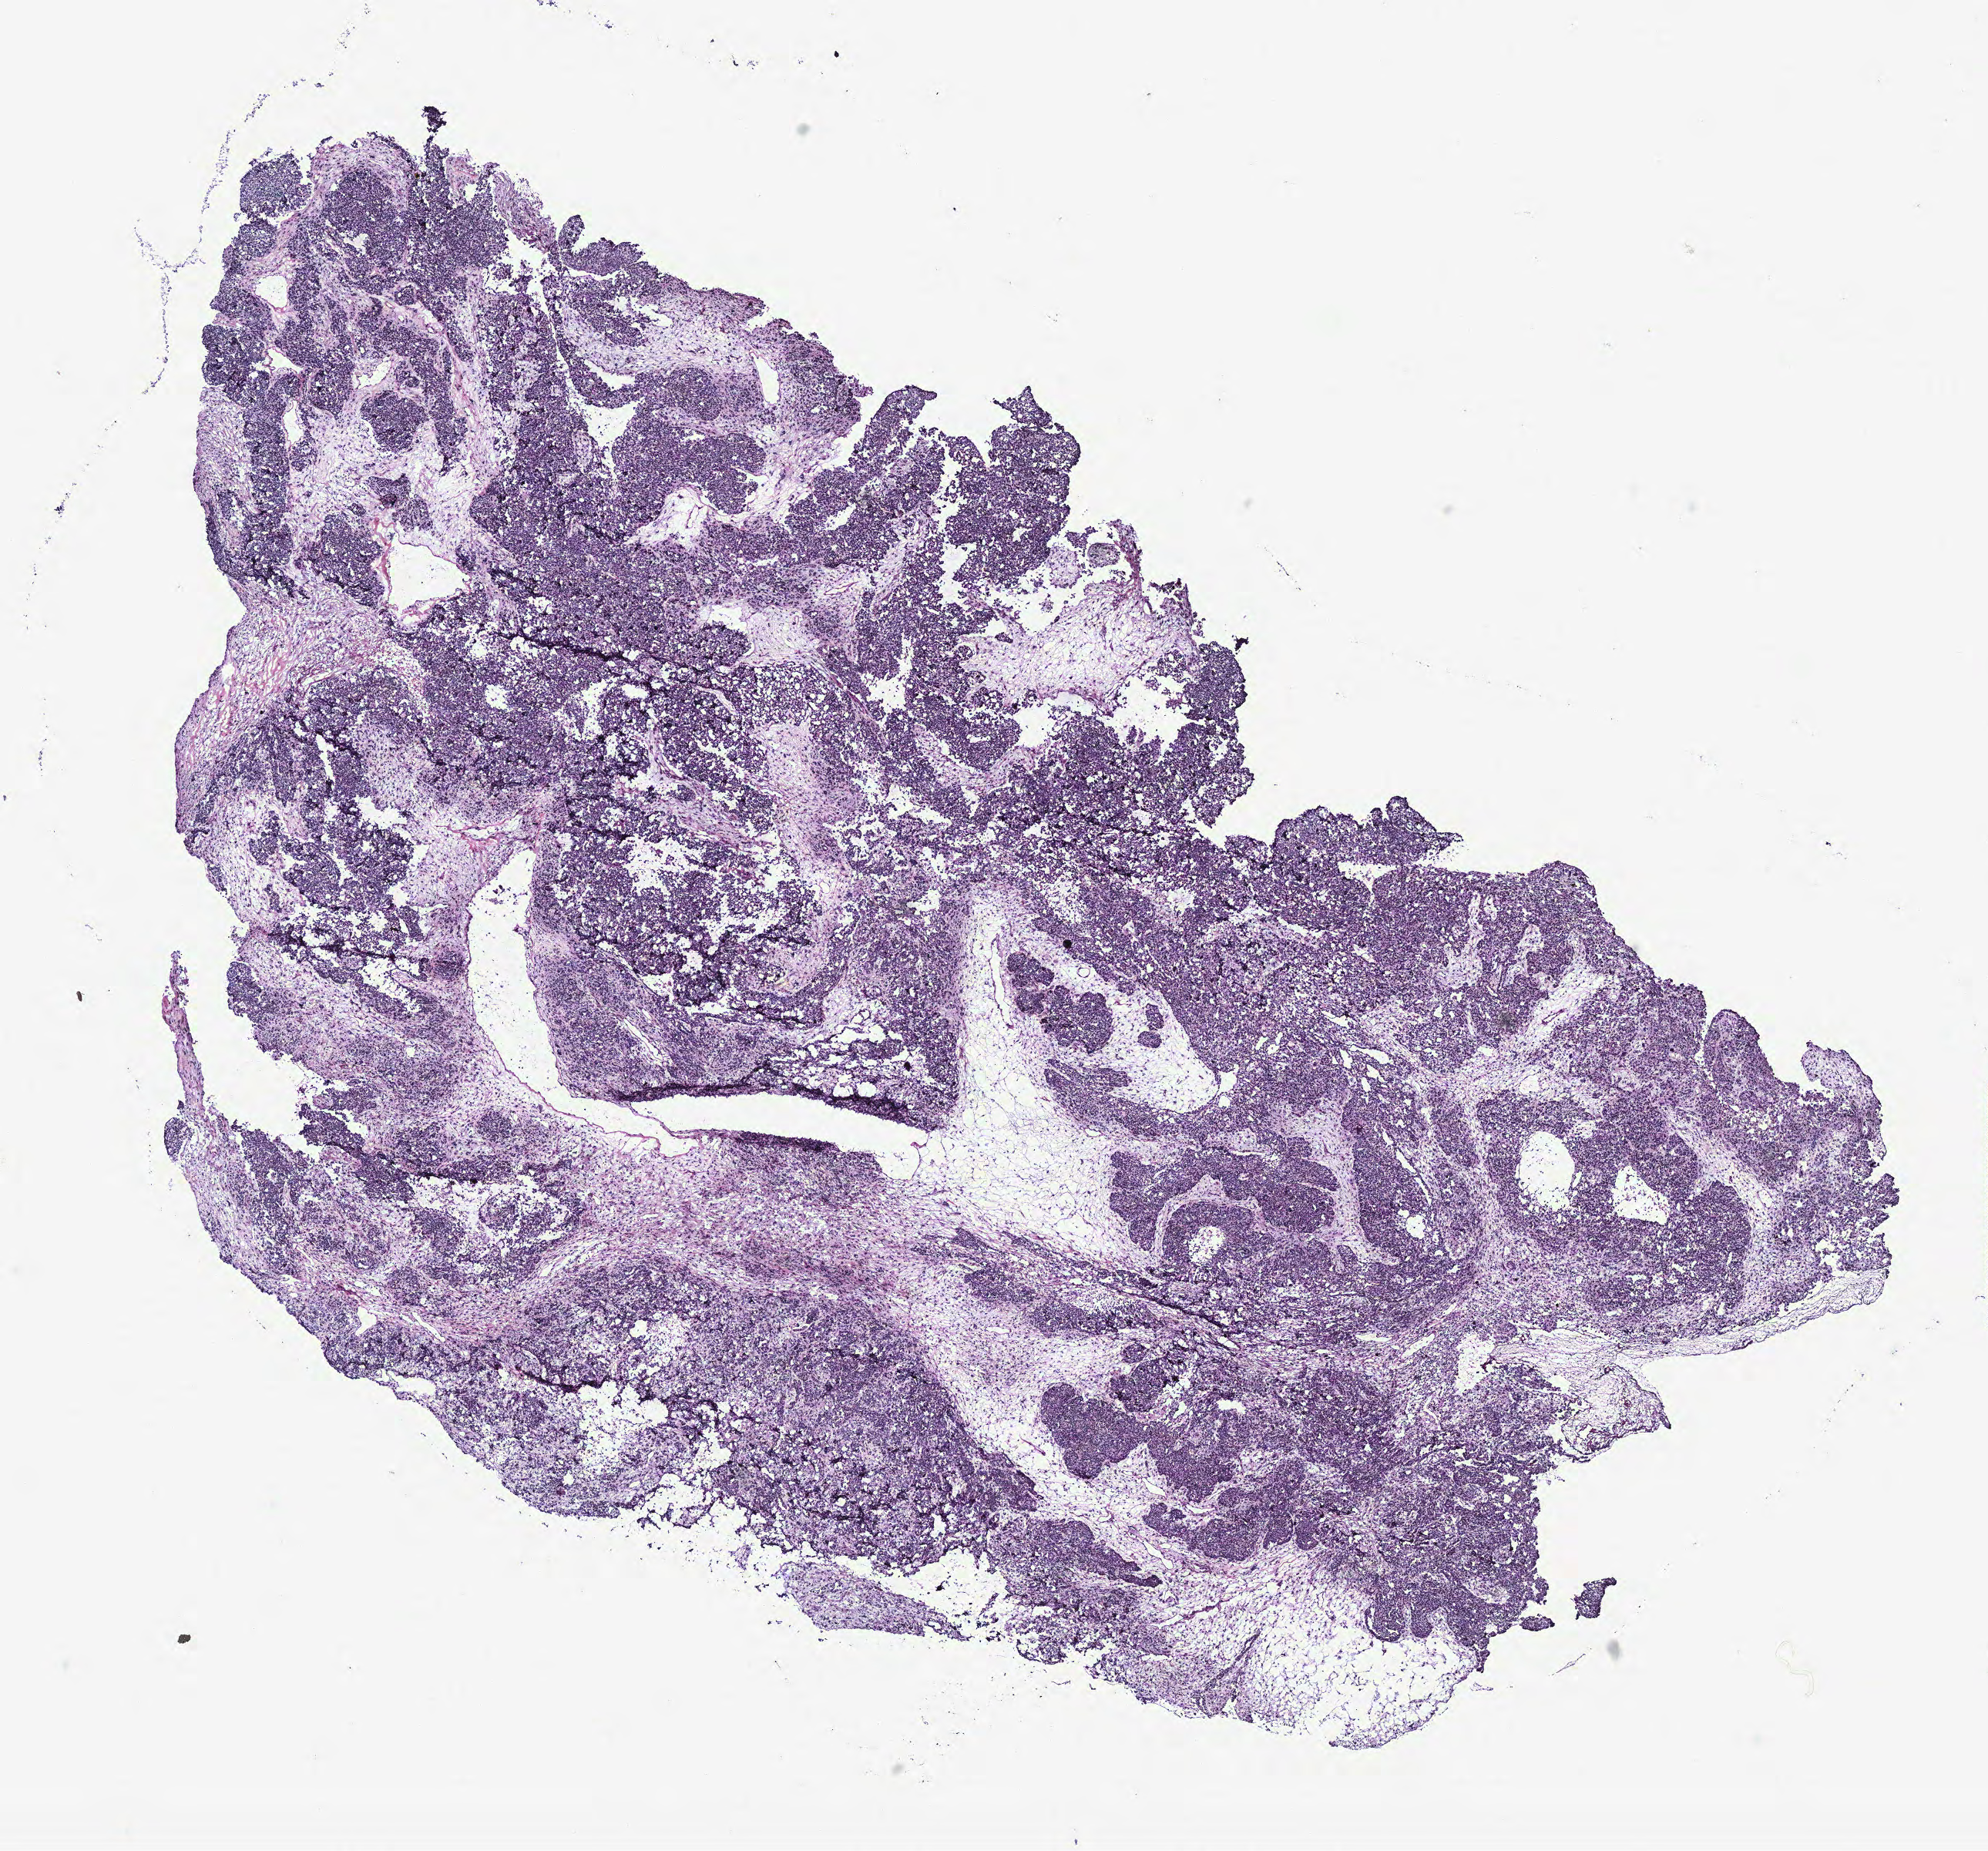
Whole-slide histology image, H&E-stained — shown as a low-resolution overview of the whole scanned area (about 10.3 x 9.6 mm). Ovary, tissue type not recorded. Female patient.
Patient diagnosis: Serous adenocarcinoma, NOS.